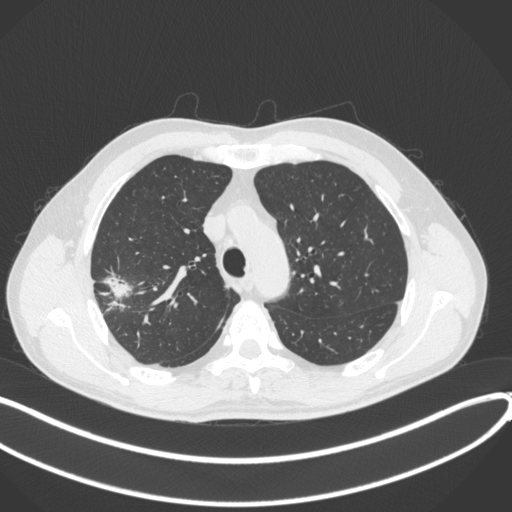
Chest CT, one axial slice; slice 310 of 381 in the series (ordered by position); lung window (W 1500 / L -600 HU); 1 mm slice thickness; 512 × 512 image matrix. Patient: male, 62 years. From the clinical record (not read from this slice): clinical TNM (as recorded): T1c N0 M0.
Outlined on this slice (rectangle marked by the reading radiologist):
- lung tumour (recorded histology: adenocarcinoma): bounding box <101,271,132,308> (left, top, right, bottom; pixels)